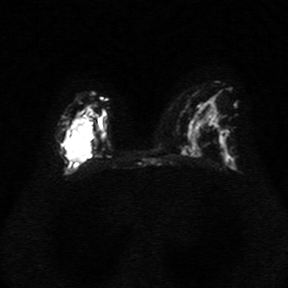
Breast MRI, one axial slice; position 20 of 34 along the scan axis; diffusion-weighted series; image 2 of 4 stored at this slice position (different b-values; order by instance number); 1.5 T; 5 mm slice thickness; 288 × 288 image matrix, field of view 340 × 340 mm. Female patient.
Annotated regions visible in this slice (expert manual segmentation):
- tumour on diffusion-weighted imaging: box from (x=62, y=118) to (x=97, y=161) px